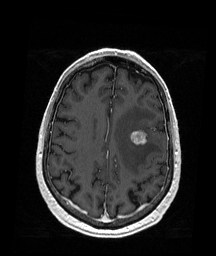
Brain MRI from a brain-tumour surgery series, one axial slice. Slice 64 of 176 in the series (ordered by position). T1-weighted post-contrast. 1 mm slice thickness. 216 × 256 image matrix. Case-level facts recorded for this patient, not image findings: histopathology: Metastatic Melanoma.
Outlined on this slice (expert manual segmentation):
- tumour: bounding box (x1, y1, x2, y2) in pixels: (130, 130, 148, 145)